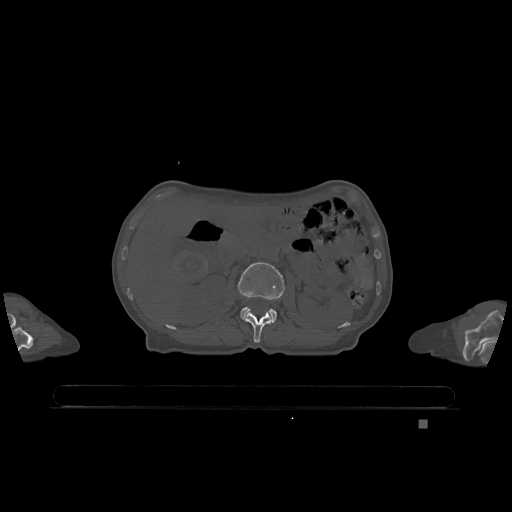
CT including the spine, one axial slice. Slice 445 of 1317 in the series (ordered by position). Bone window (W 1800 / L 400 HU). 0.5 mm slice thickness. 512 × 512 image matrix, field of view 500 × 500 mm. Female patient, age 74 years. Case-level facts recorded for this patient, not image findings: primary cancer: lung.
Annotated regions visible in this slice (semi-automatic segmentation, software-assisted and operator-edited):
- L1 vertebra: bounding box <244,312,272,343> (left, top, right, bottom; pixels)
- L2 vertebra: <238,262,285,323>